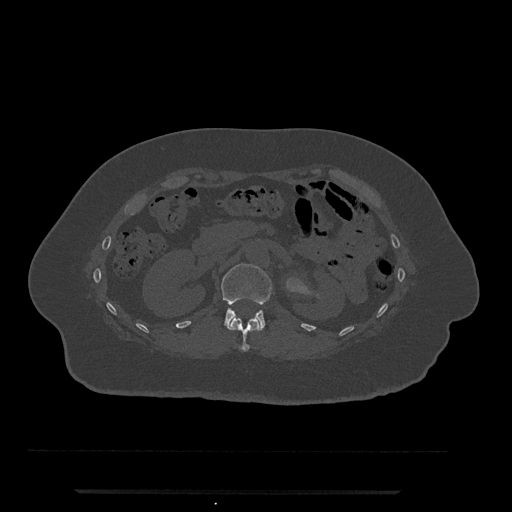
CT including the spine, one axial slice. Position 130 of 797 along the scan axis. 120 kVp. Bone window (W 1800 / L 400 HU). 0.5 mm slice thickness. 512 × 512 image matrix, field of view 440 × 440 mm. Patient: female, 51 years. Case-level facts recorded for this patient, not image findings: primary cancer: neuro; vertebrae with lytic lesions (as recorded): T8.
Structures marked on this image (semi-automatic segmentation, software-assisted and operator-edited):
- L1 vertebra: box from (x=221, y=263) to (x=273, y=329) px
- T12 vertebra: (x=228, y=318)–(x=262, y=352)